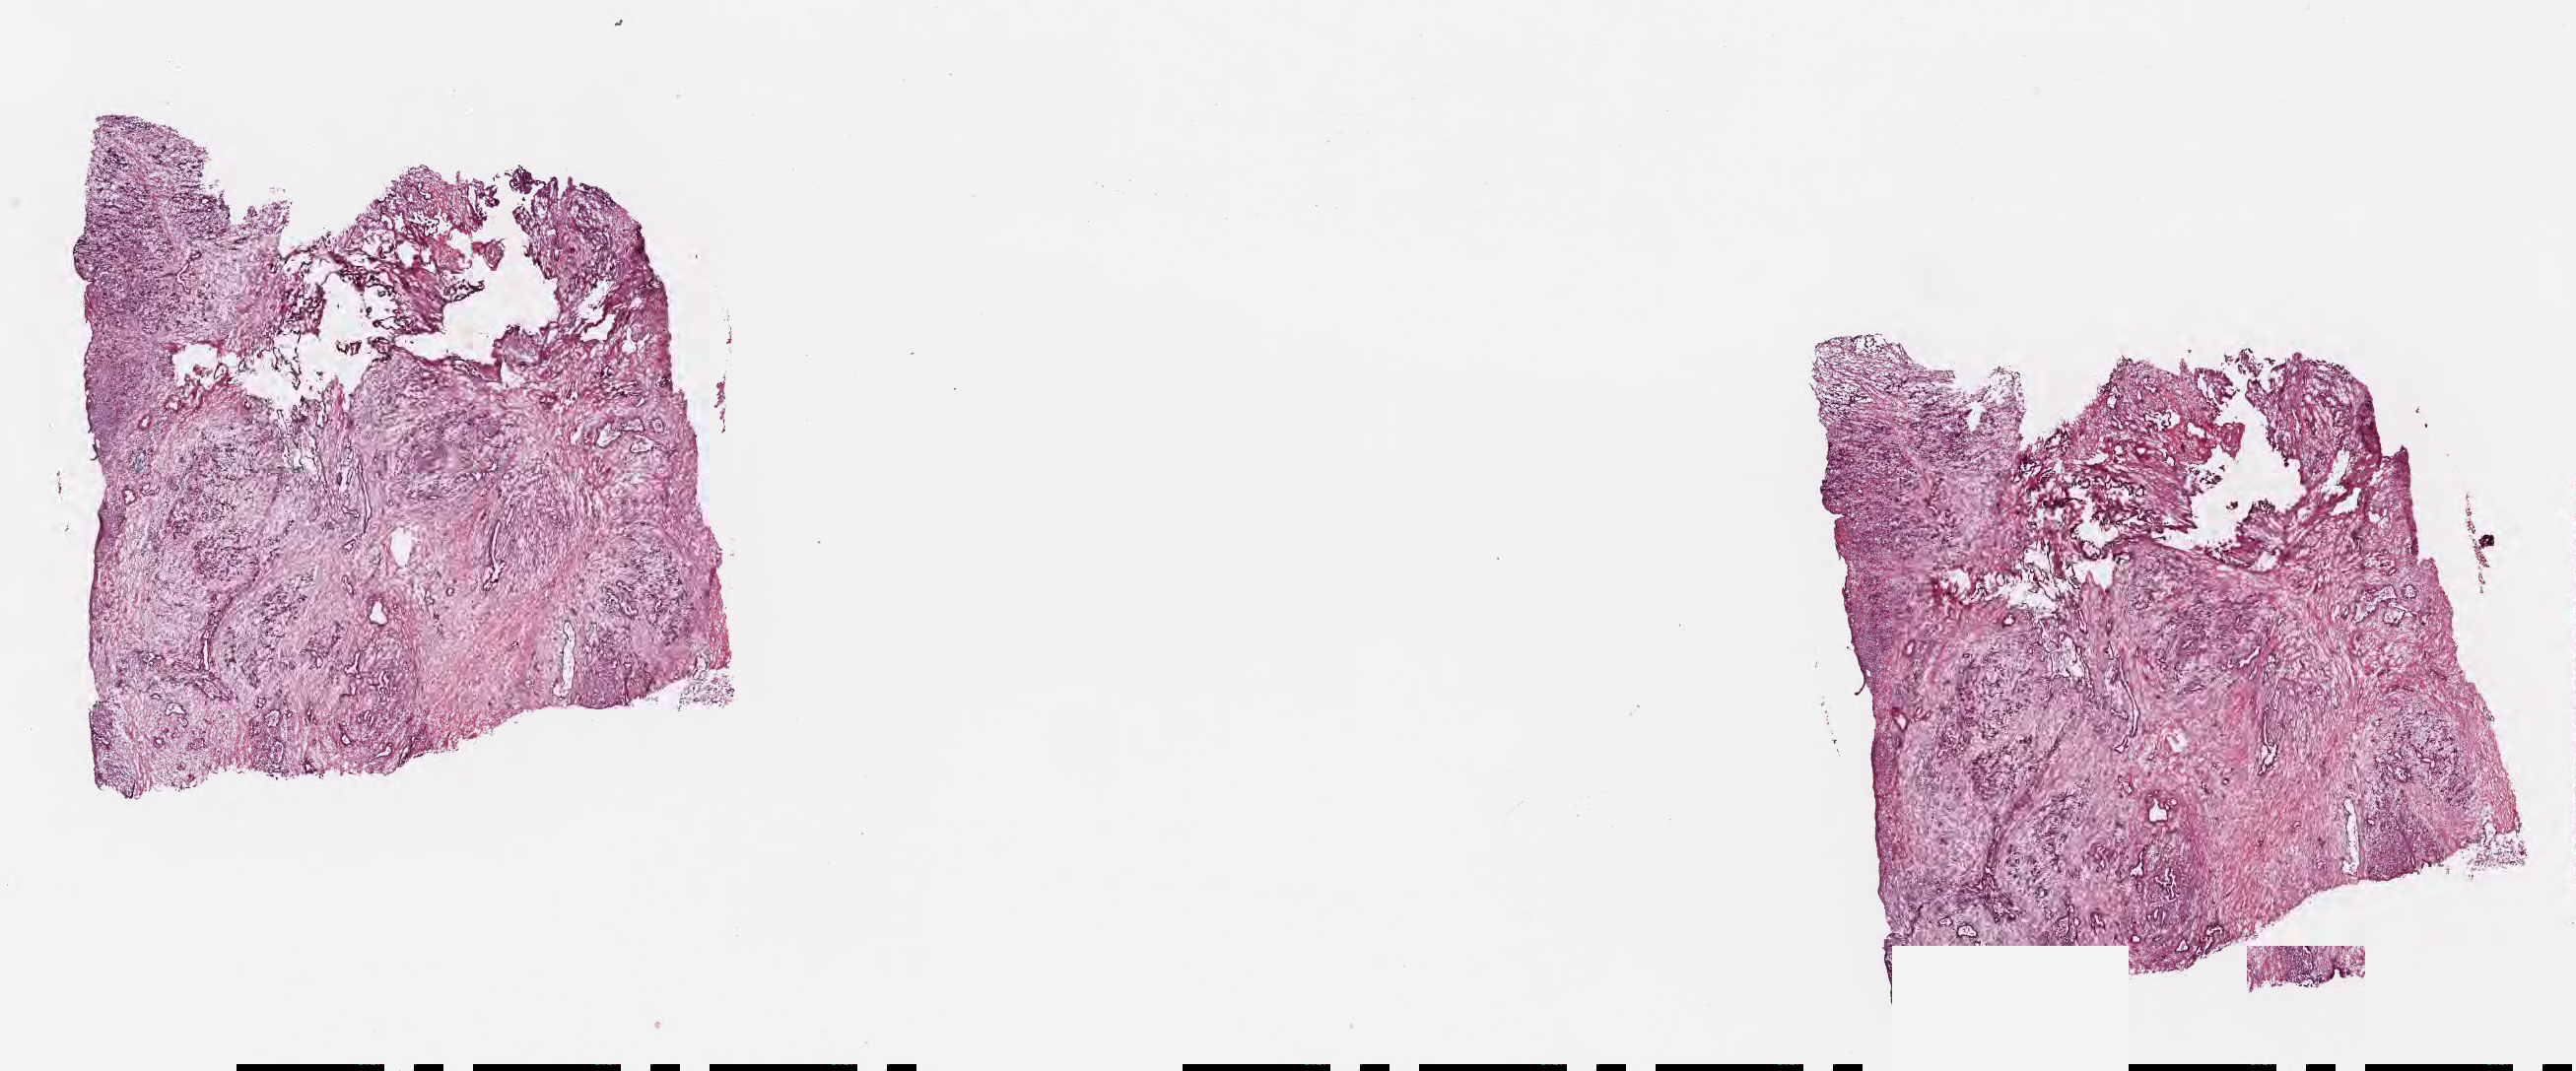
H&E whole-slide image, shown as a low-resolution overview of the whole scanned area (about 21.1 x 8.8 mm), frozen section, primary tumor, site: head of pancreas. Female, age 63 years at initial diagnosis. Tumor grade: G2 (moderately differentiated). Slide review estimates, as recorded: tumor cells 30%, tumor nuclei 40%, stromal cells 70%, necrosis 0%, normal cells 0%. Infiltration values recorded for this section: lymphocyte infiltration 0%, monocyte infiltration 0%, neutrophil infiltration 0%.
* AJCC pathologic stage: Stage IIB
* diagnosis: Infiltrating duct carcinoma, NOS